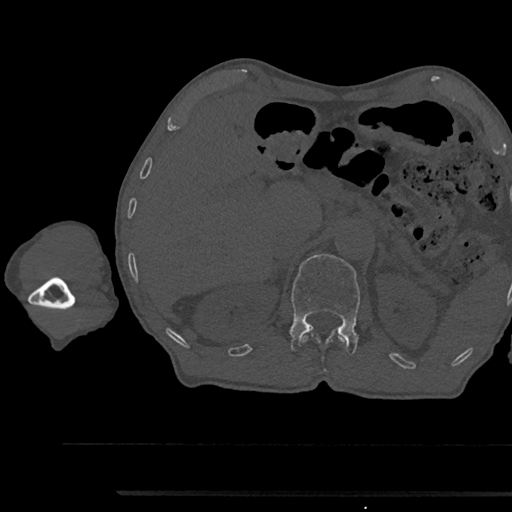
CT including the spine, one axial slice; position 666 of 797 along the scan axis; reconstruction kernel Br40s/3; 120 kVp; bone window (W 1800 / L 400 HU); 0.5 mm slice thickness; 512 × 512 image matrix, field of view 367 × 367 mm. Male patient, age 79 years. Case-level facts recorded for this patient, not image findings: primary cancer: prostate.
Structures marked on this image (semi-automatic segmentation, software-assisted and operator-edited):
- L1 vertebra: bounding box [x1, y1, x2, y2] px = [289, 254, 360, 354]
- T12 vertebra: [303, 333, 343, 343]